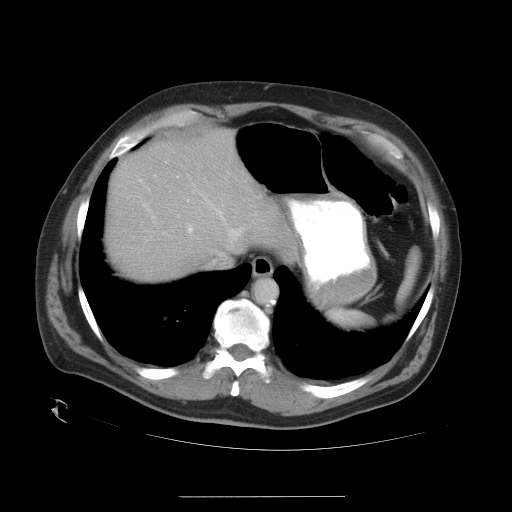
Contrast-enhanced abdominal CT, one axial slice. Slice 28 of 35 in the series (ordered by position). Reconstruction kernel STANDARD. 120 kVp. Intravenous contrast given. Soft-tissue window (W 400 / L 40 HU). 7.5 mm slice thickness. 512 × 512 image matrix. Male patient, age 67 years. From the clinical record (not read from this slice): diagnosis: colorectal cancer liver metastases, imaged before liver resection; multiple liver metastases: no; largest metastasis: 2.3 cm; disease in both lobes: no.
Structures marked on this image (outlined manually by an expert reader):
- hepatic veins: bounding box <138,174,241,239> (left, top, right, bottom; pixels)
- liver: <106,132,288,279>
- planned liver remnant (the part of the liver to remain after resection): <110,132,288,279>
- portal vein (with intrahepatic branches): <177,174,193,233>